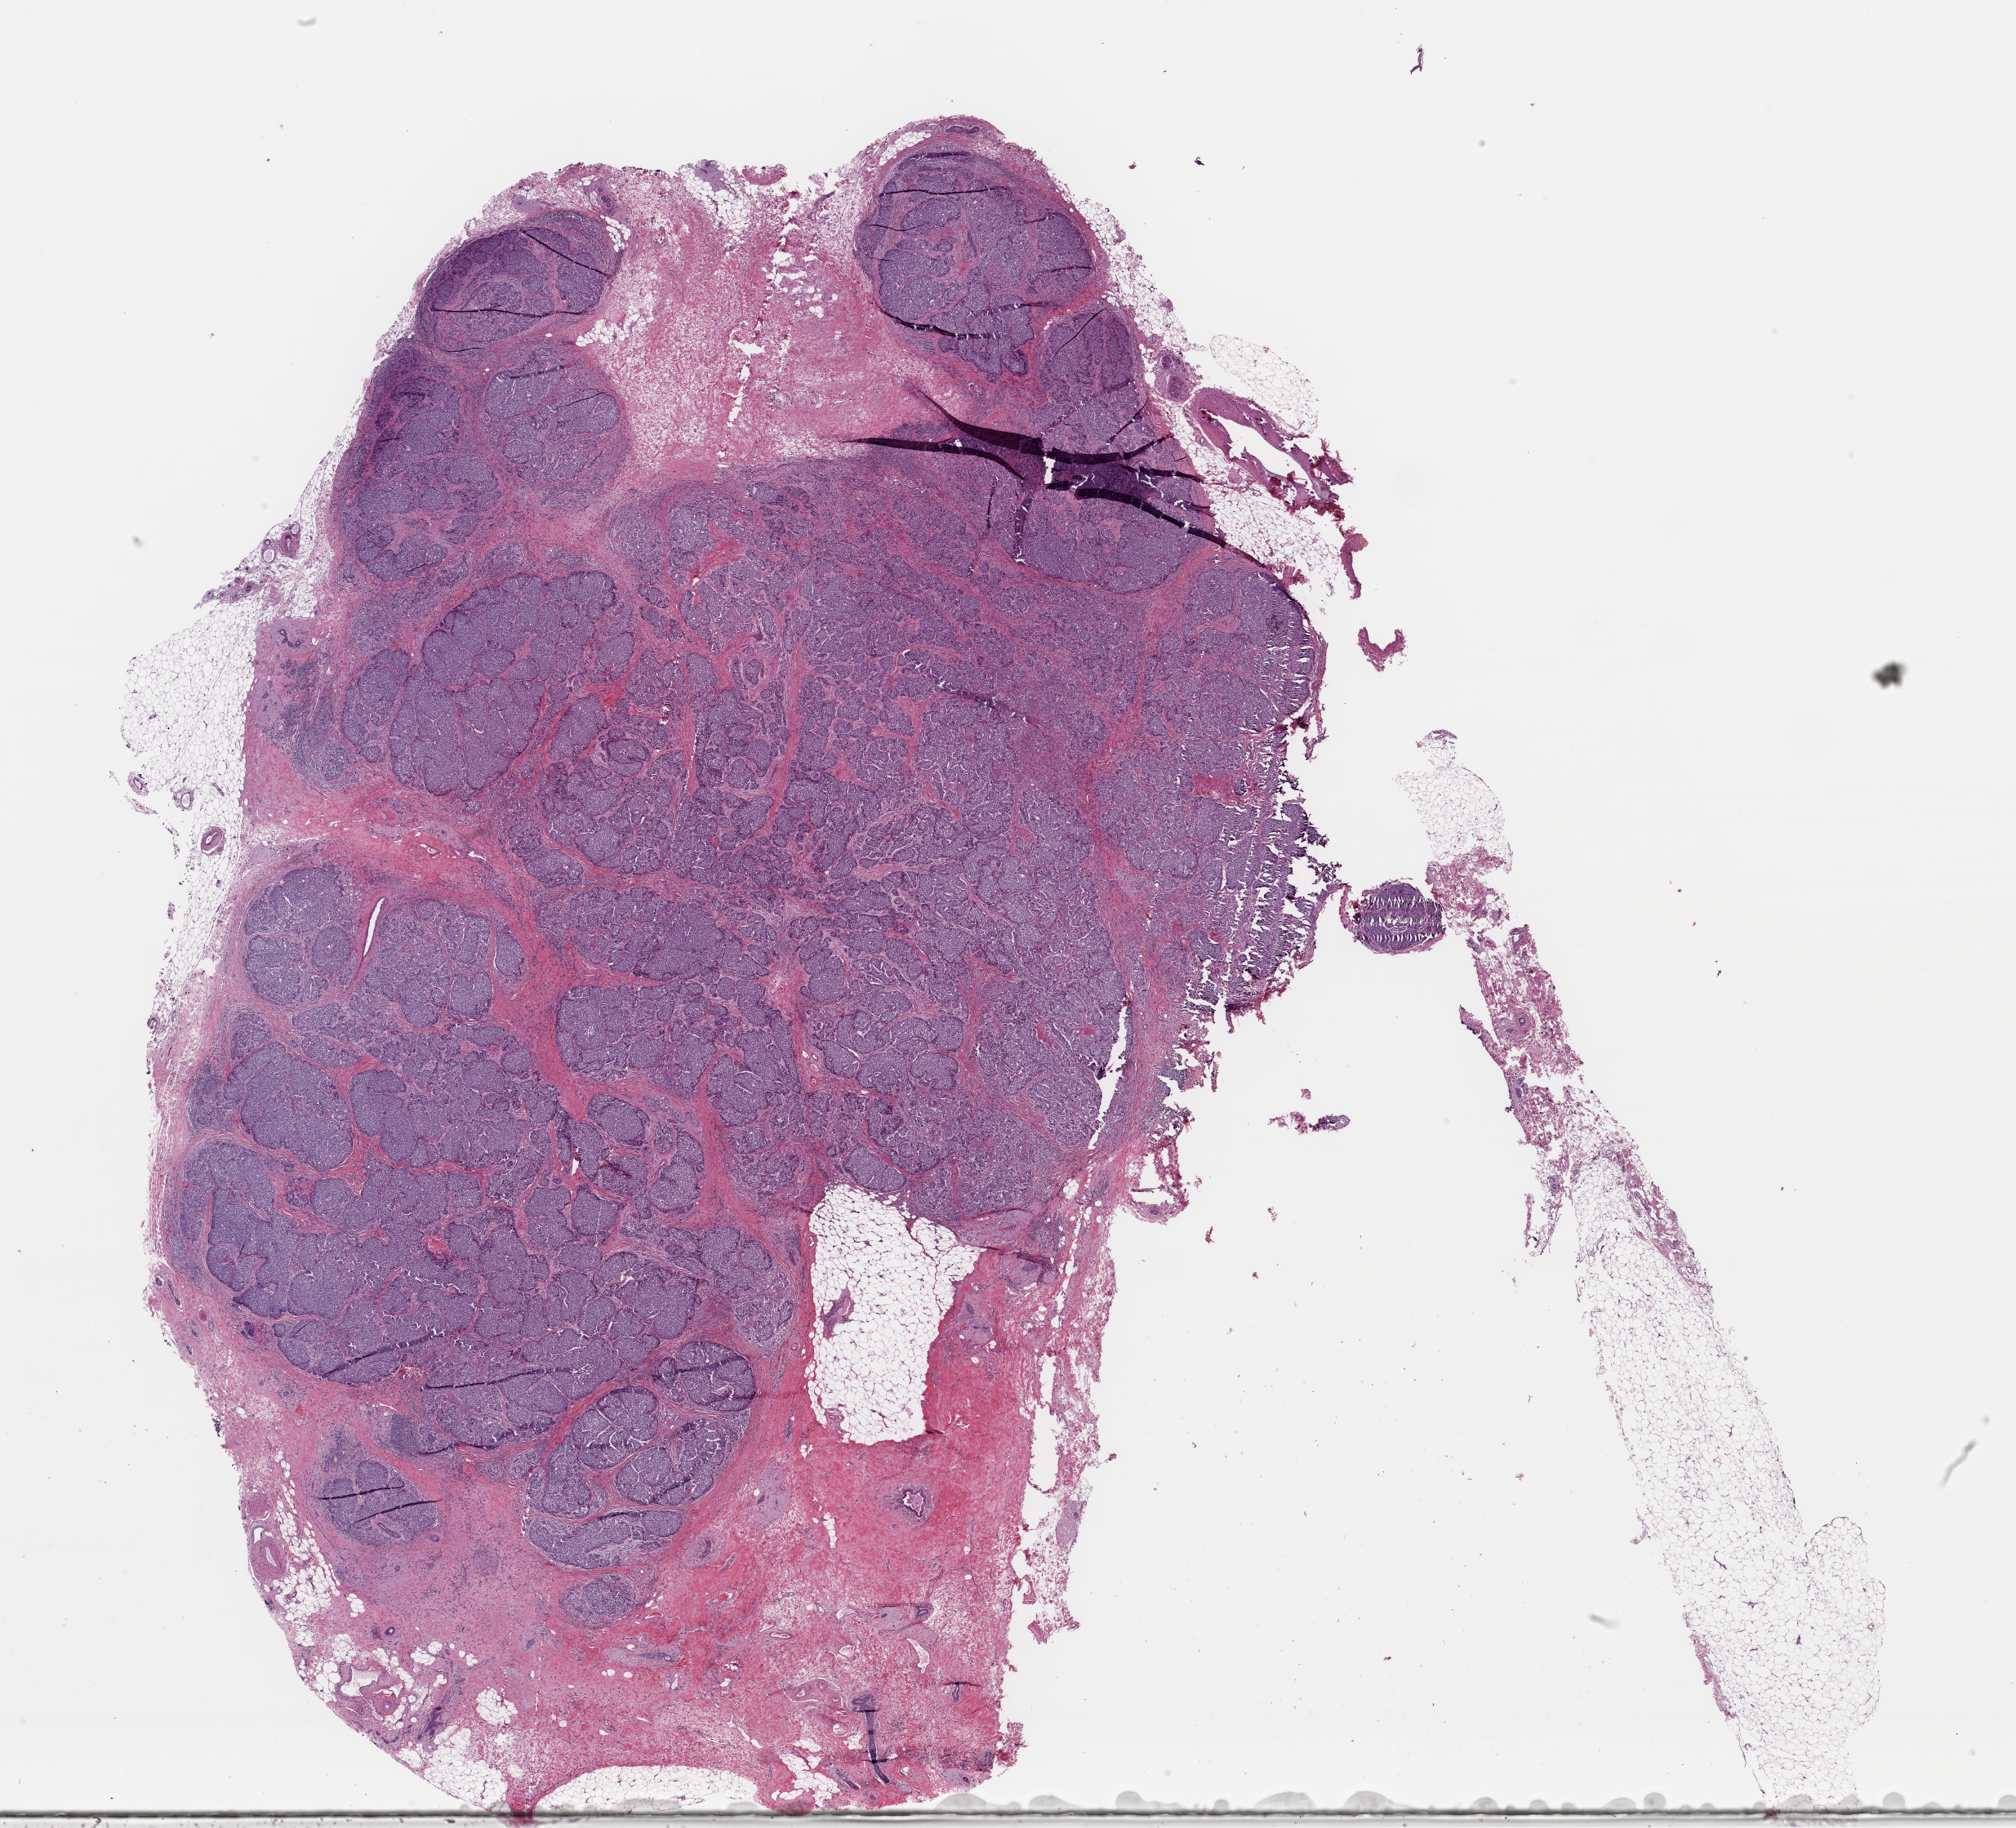
Hematoxylin and eosin (H&E) stained whole-slide image — whole scanned area (about 19.5 x 17.7 mm) shown as a low-resolution overview; FFPE section; primary tumour sample from the breast. Female patient; age at initial diagnosis 66 years.
Lymph nodes positive (case pathology): 0 of 3 examined. AJCC pathologic stage: IIA (6th edition). Histologic diagnosis: Infiltrating duct carcinoma, NOS.